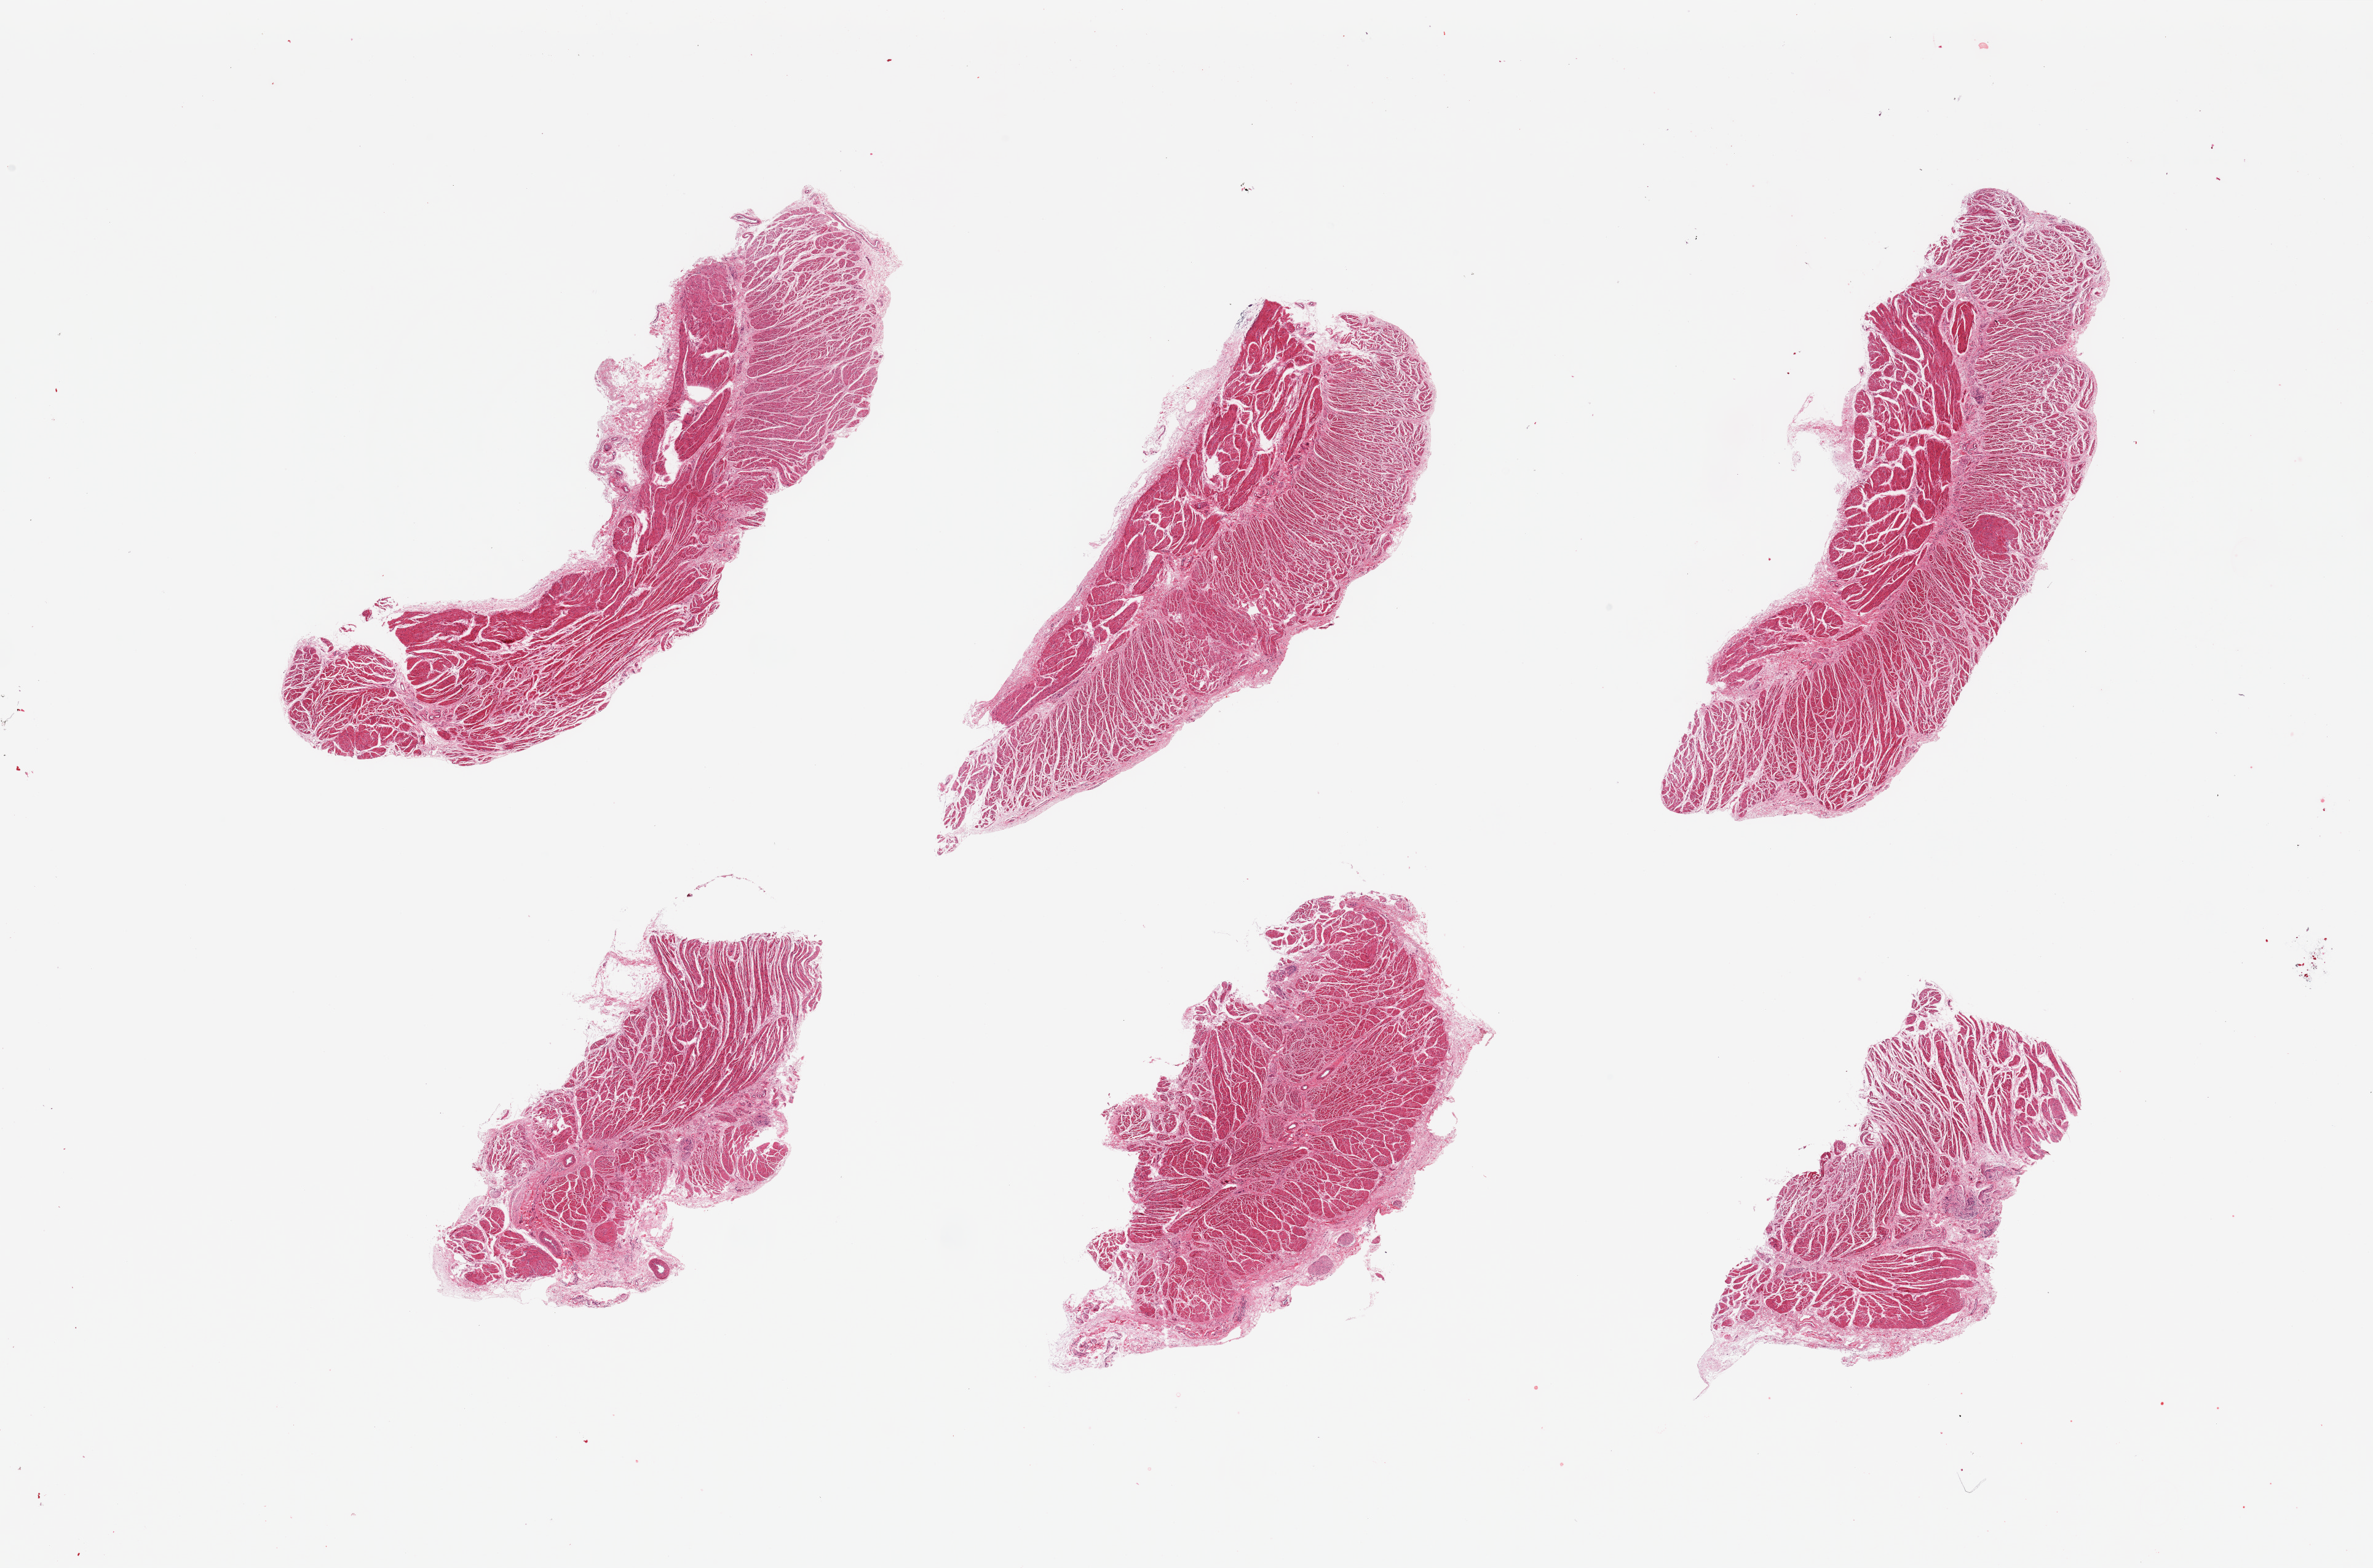
Digitized haematoxylin and eosin-stained section, shown as a low-resolution overview of the whole scanned area (about 30.5 x 20.2 mm); PAXgene-fixed, paraffin-embedded tissue; sampled site (target tissue): gastroesophageal junction; donor tissue sample. Male donor.
Pathologist's review note for this sample: 6 pieces; target muscularis with small leiomyoma.